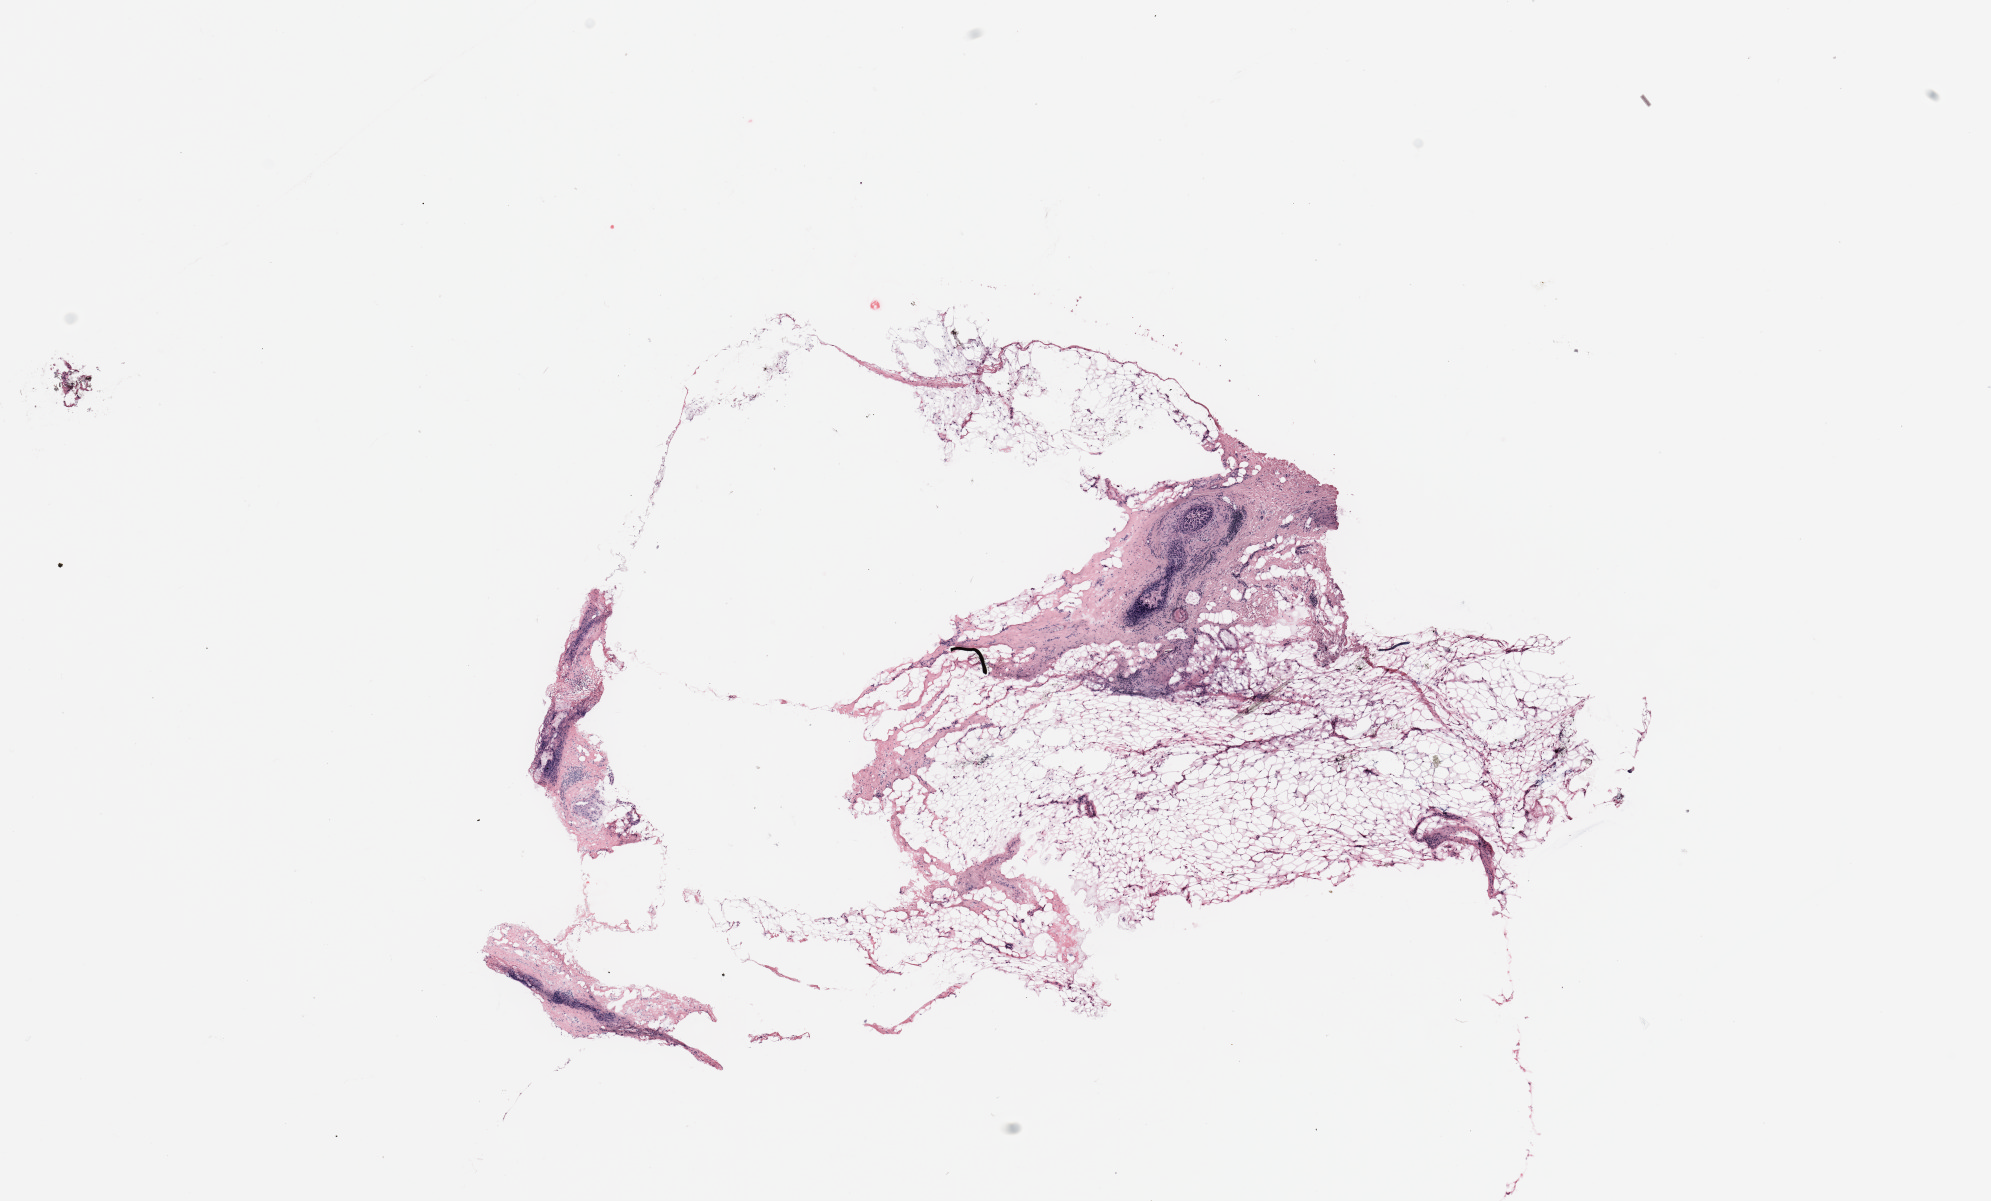
Whole-slide histology image, H&E-stained — whole scanned area (about 15.8 x 9.5 mm, from a 20x scan) shown as a low-resolution overview, tumour tissue sample, breast. Female, 71 y/o.
Diagnosis: Intraductal papillary carcinoma.